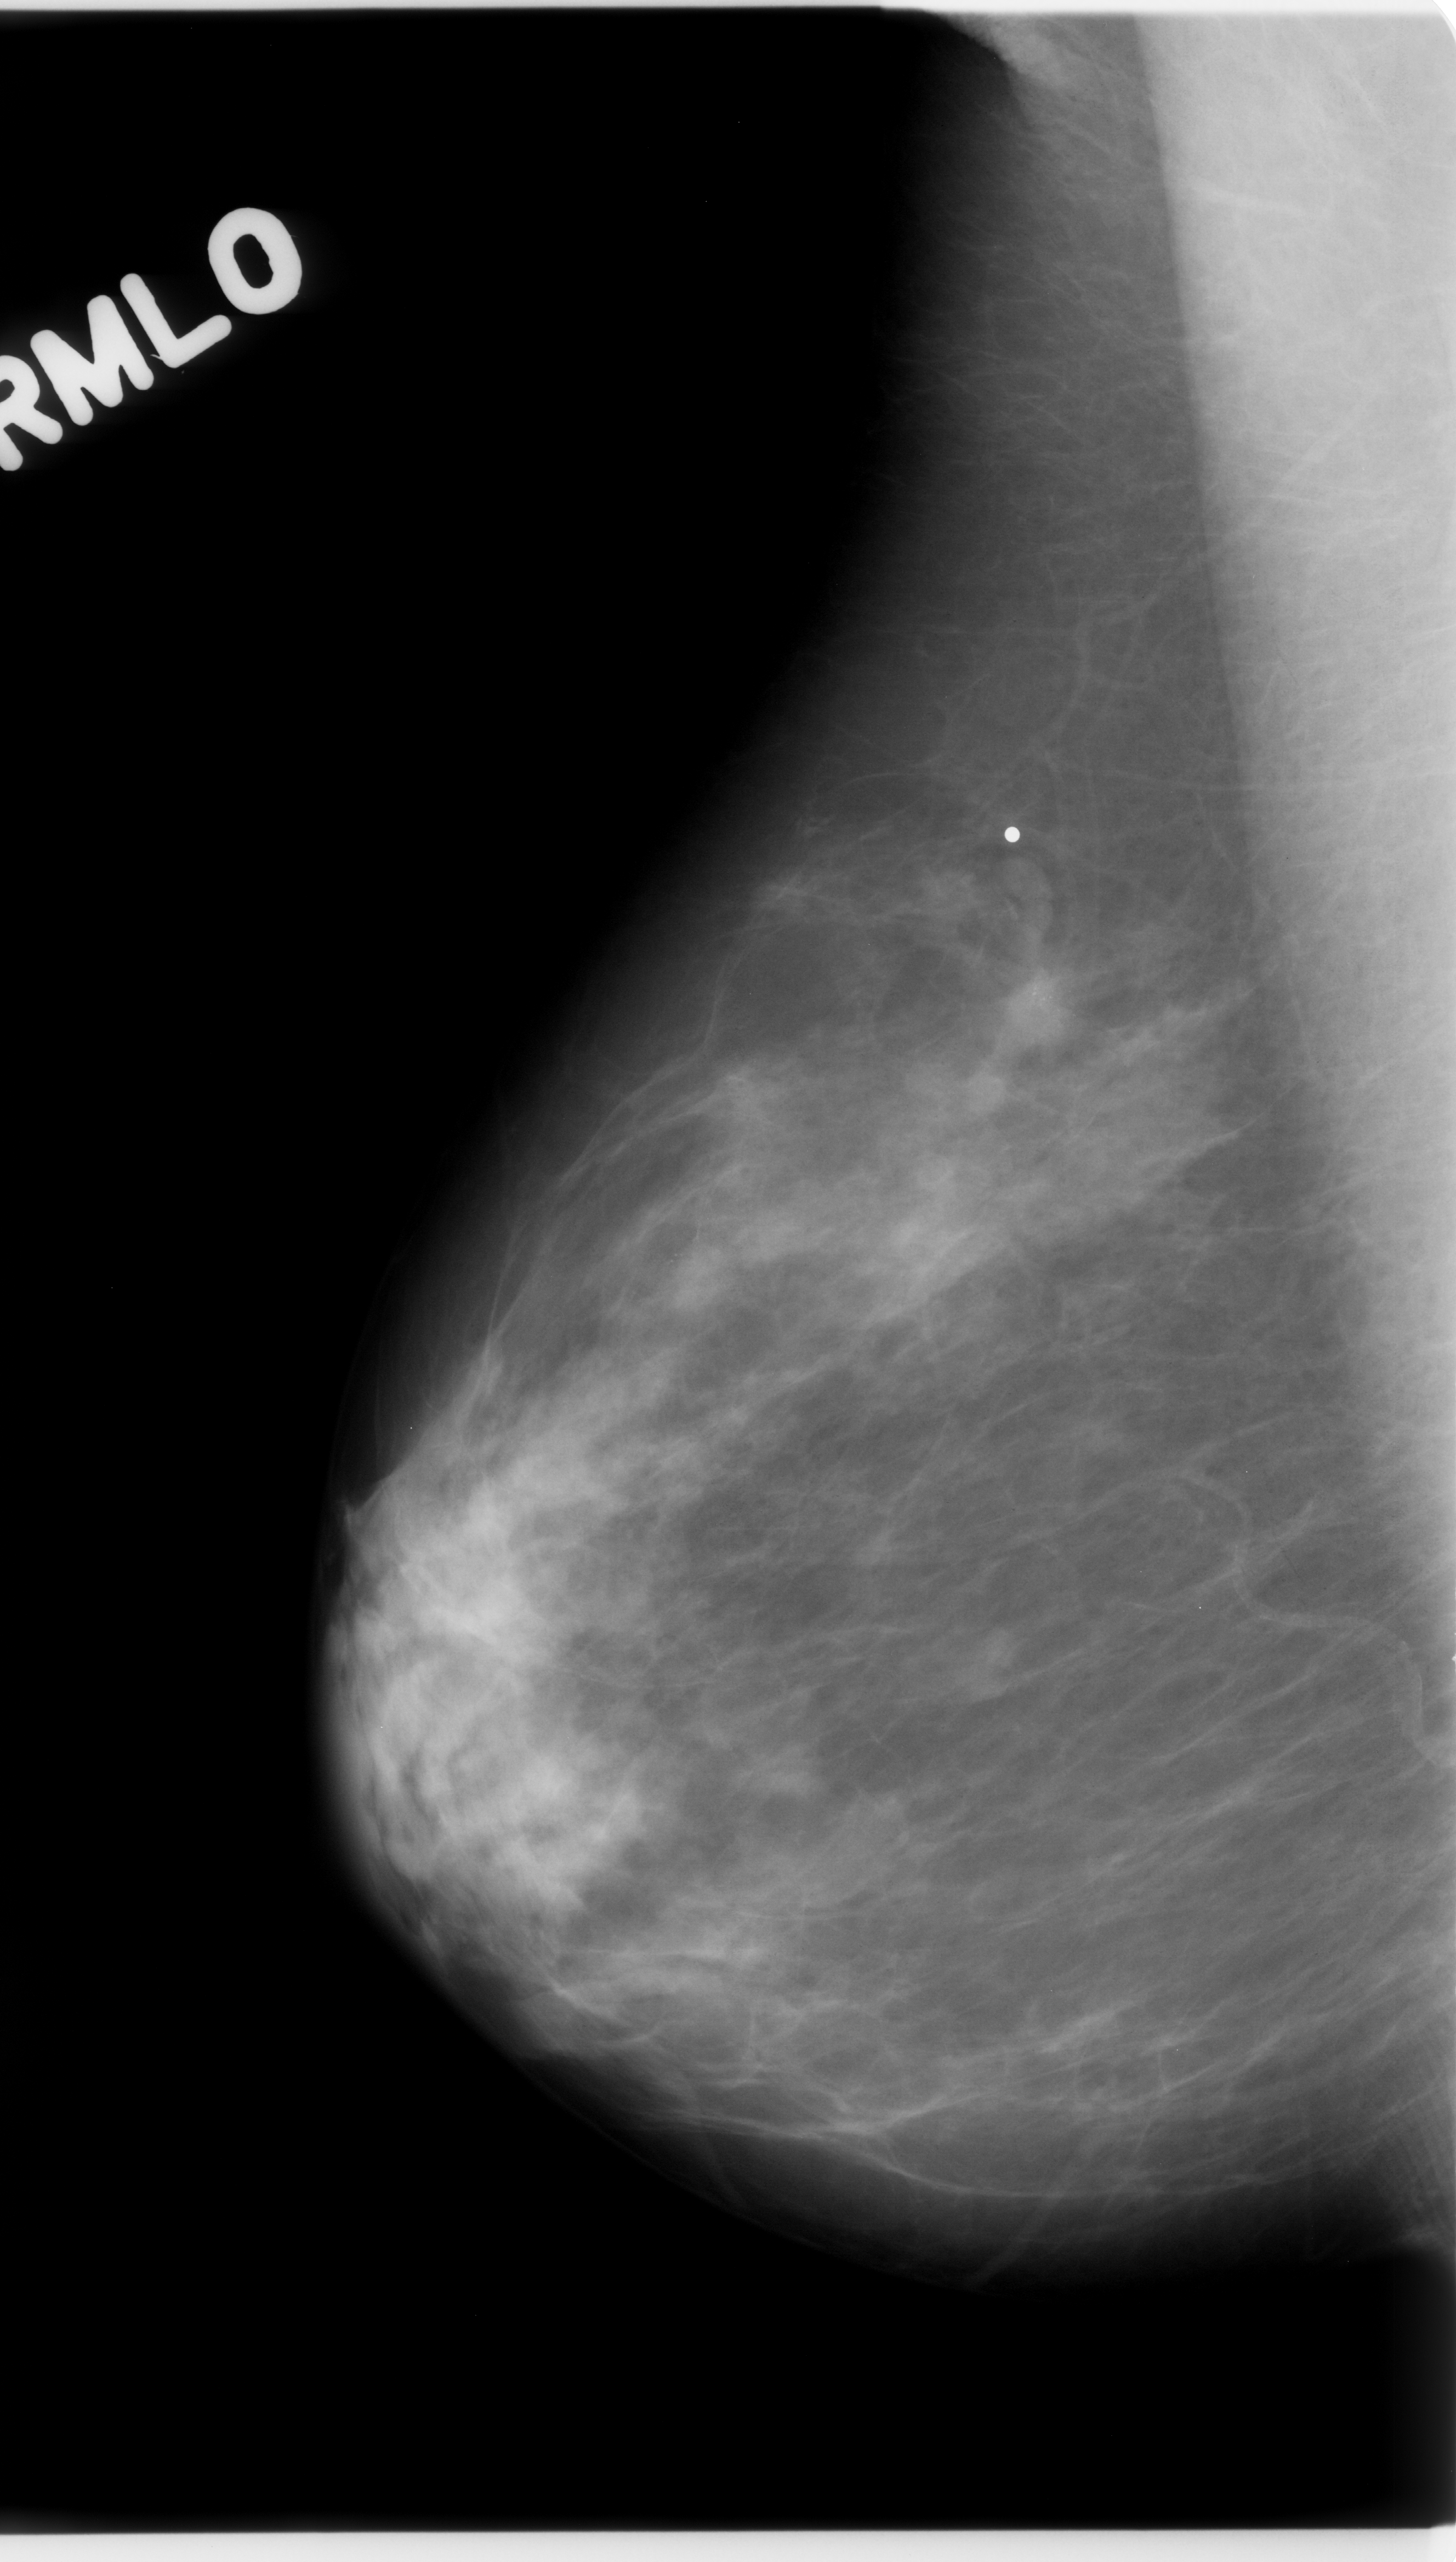
Scanned film-screen mammogram. Right breast. MLO view. BI-RADS breast density category 2 (scale 1–4). 1456 × 2562 image matrix.
Marked abnormalities (boxes around the expert regions of interest):
- calcifications, morphology pleomorphic, distribution clustered; BI-RADS assessment category 5; pathology (as recorded): malignant: bounding box [x1, y1, x2, y2] px = [907, 877, 1172, 1164]